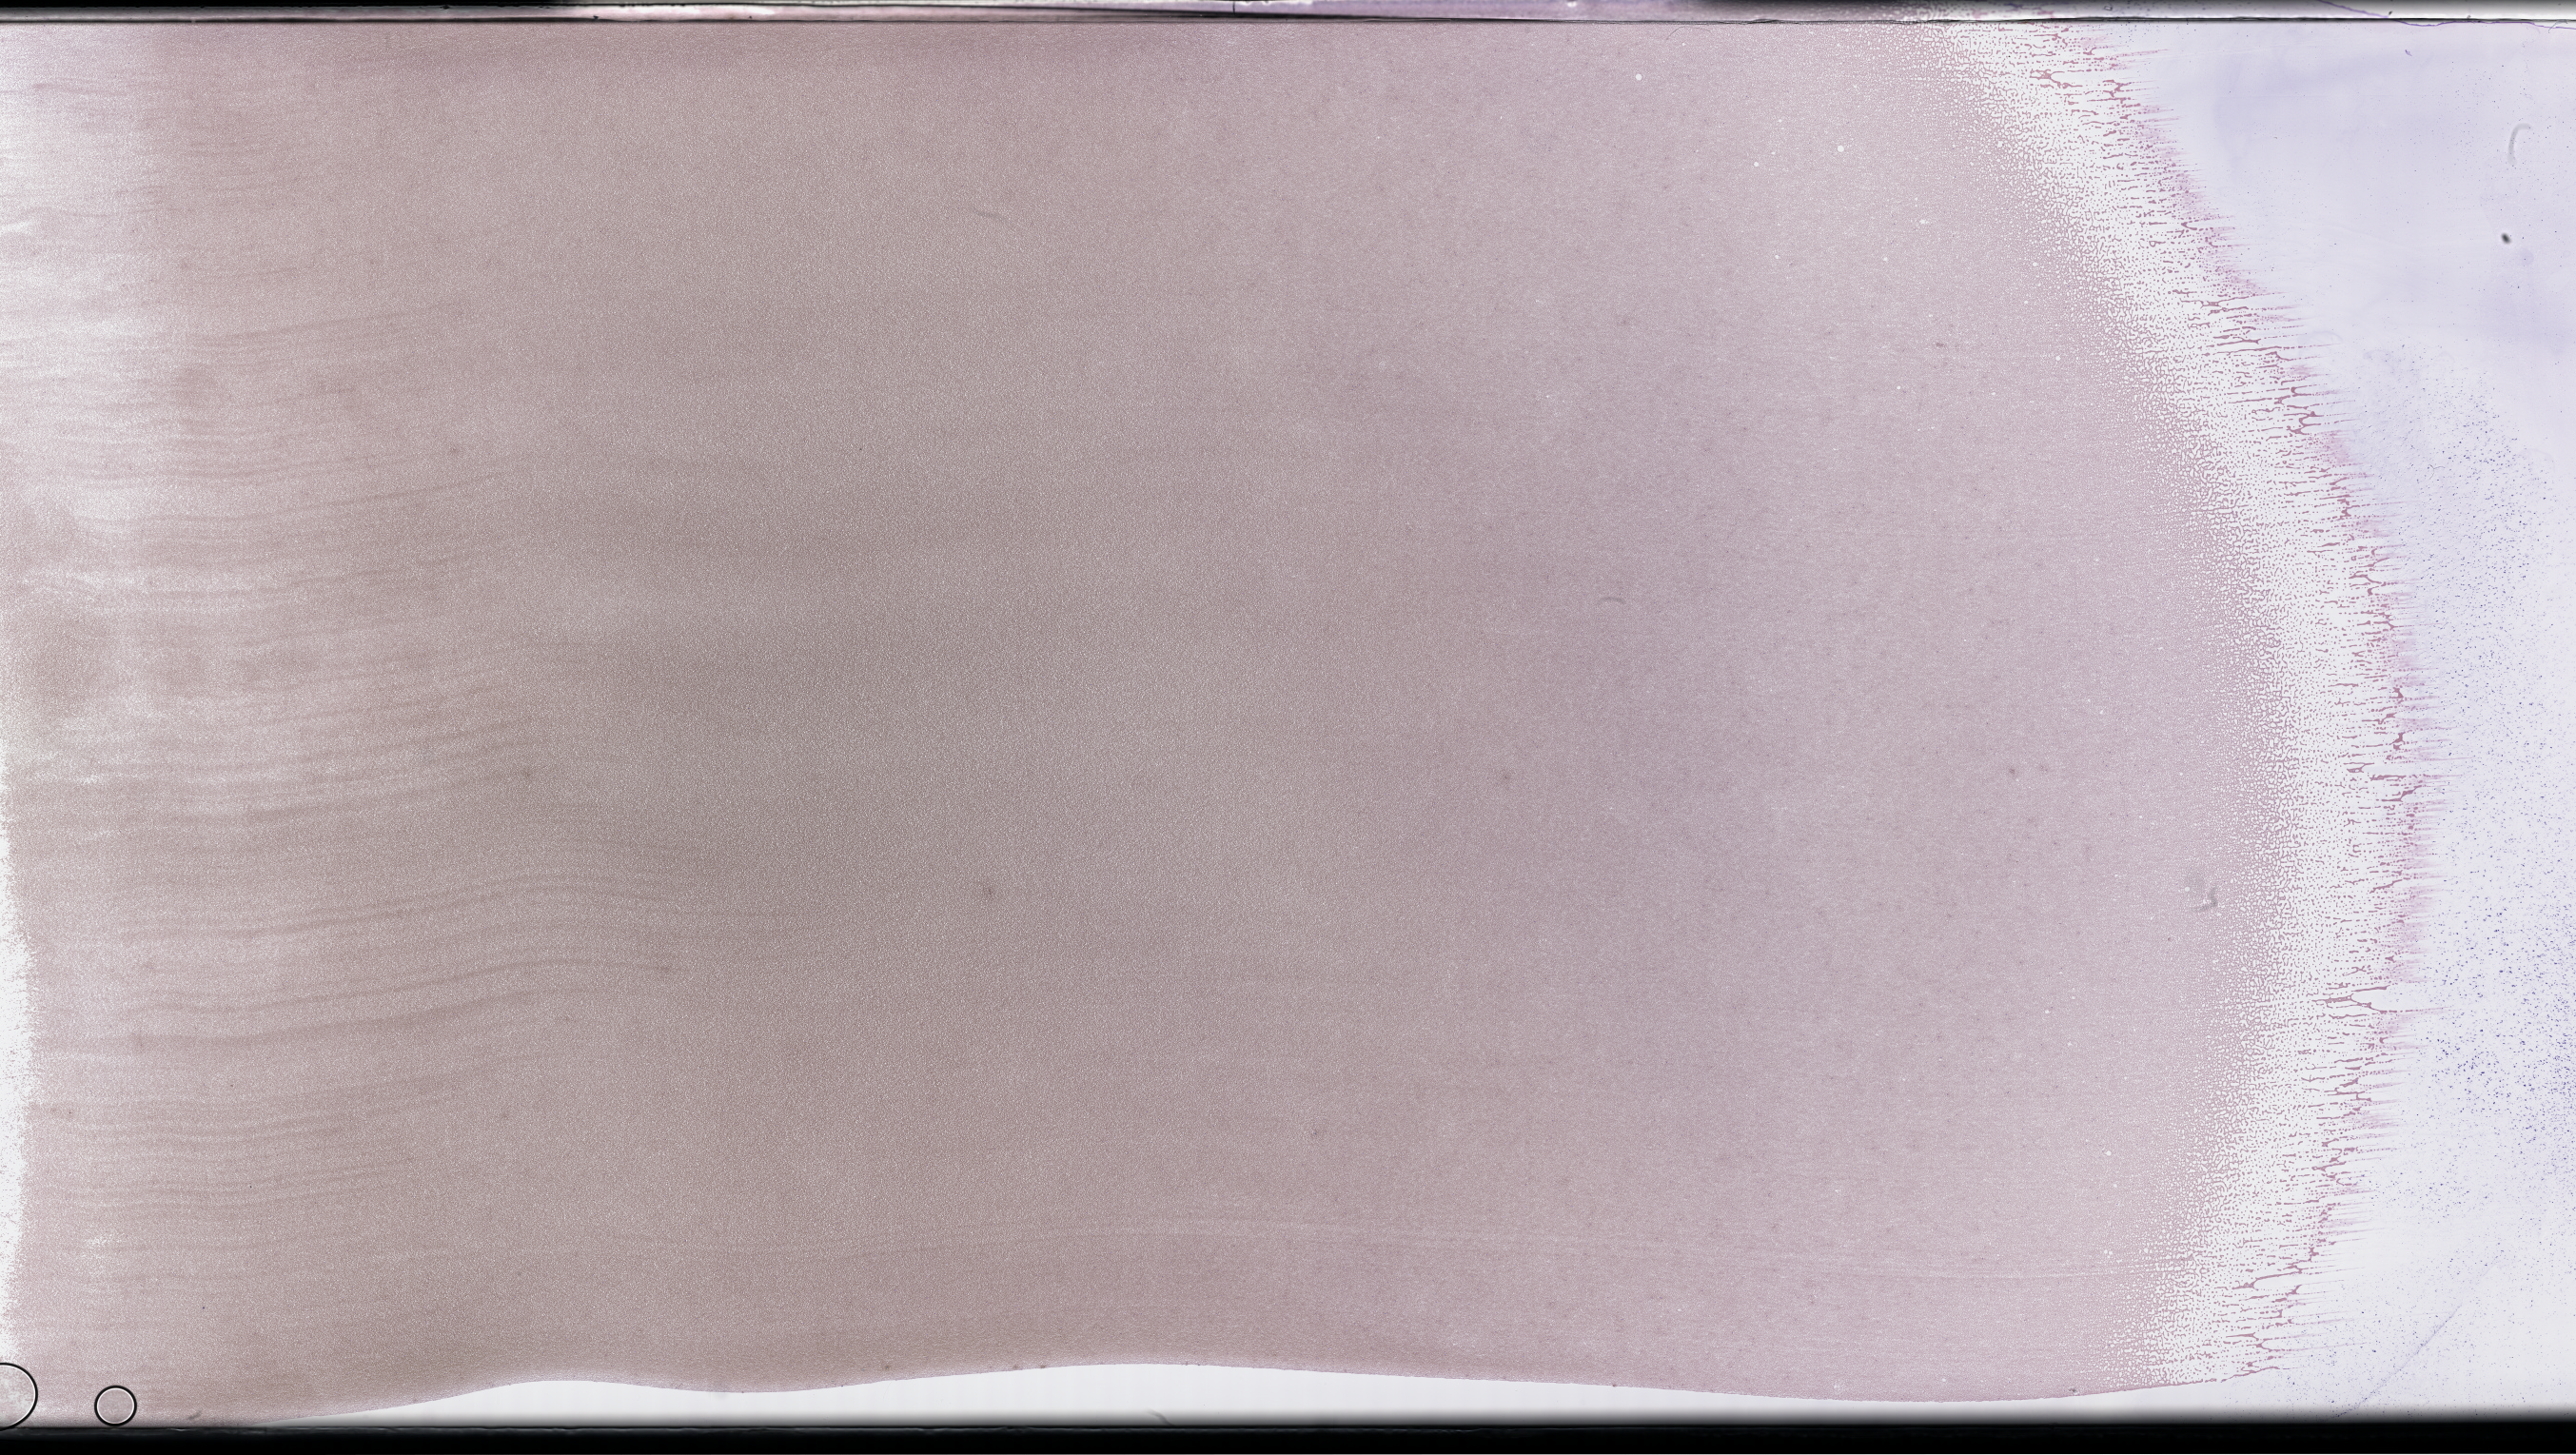
Wright–Giemsa-stained whole blood smear, whole-slide image — whole scanned area (about 43.7 x 24.7 mm) shown as a low-resolution overview, smear from an EDTA sample. Patient sex: male.
Patient diagnosis: Plasma Cell Myeloma.